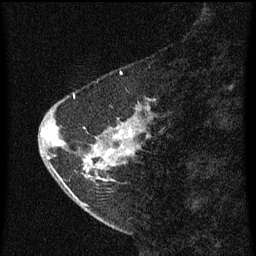
Breast MRI (dynamic contrast-enhanced), one sagittal slice; slice 18 of 60 in the series (ordered by position); dynamic contrast-enhanced series, image 2 of 3 at this slice position (ordered by acquisition); 1.5 T; TE 4.2 ms, TR 8 ms; 2 mm slice thickness; 256 × 256 image matrix, field of view 180 × 180 mm. Female patient, age 47 years.
Outlined on this slice (semi-automatically segmented with operator editing):
- analysis volume of interest (the breast-tissue region the enhancement analysis was run in; not a lesion): bounding box (x1, y1, x2, y2) in pixels: (44, 90, 153, 199)
- tumour enhancement mask (voxels above the 70 % enhancement threshold inside the analysis volume of interest): (44, 96, 139, 181)